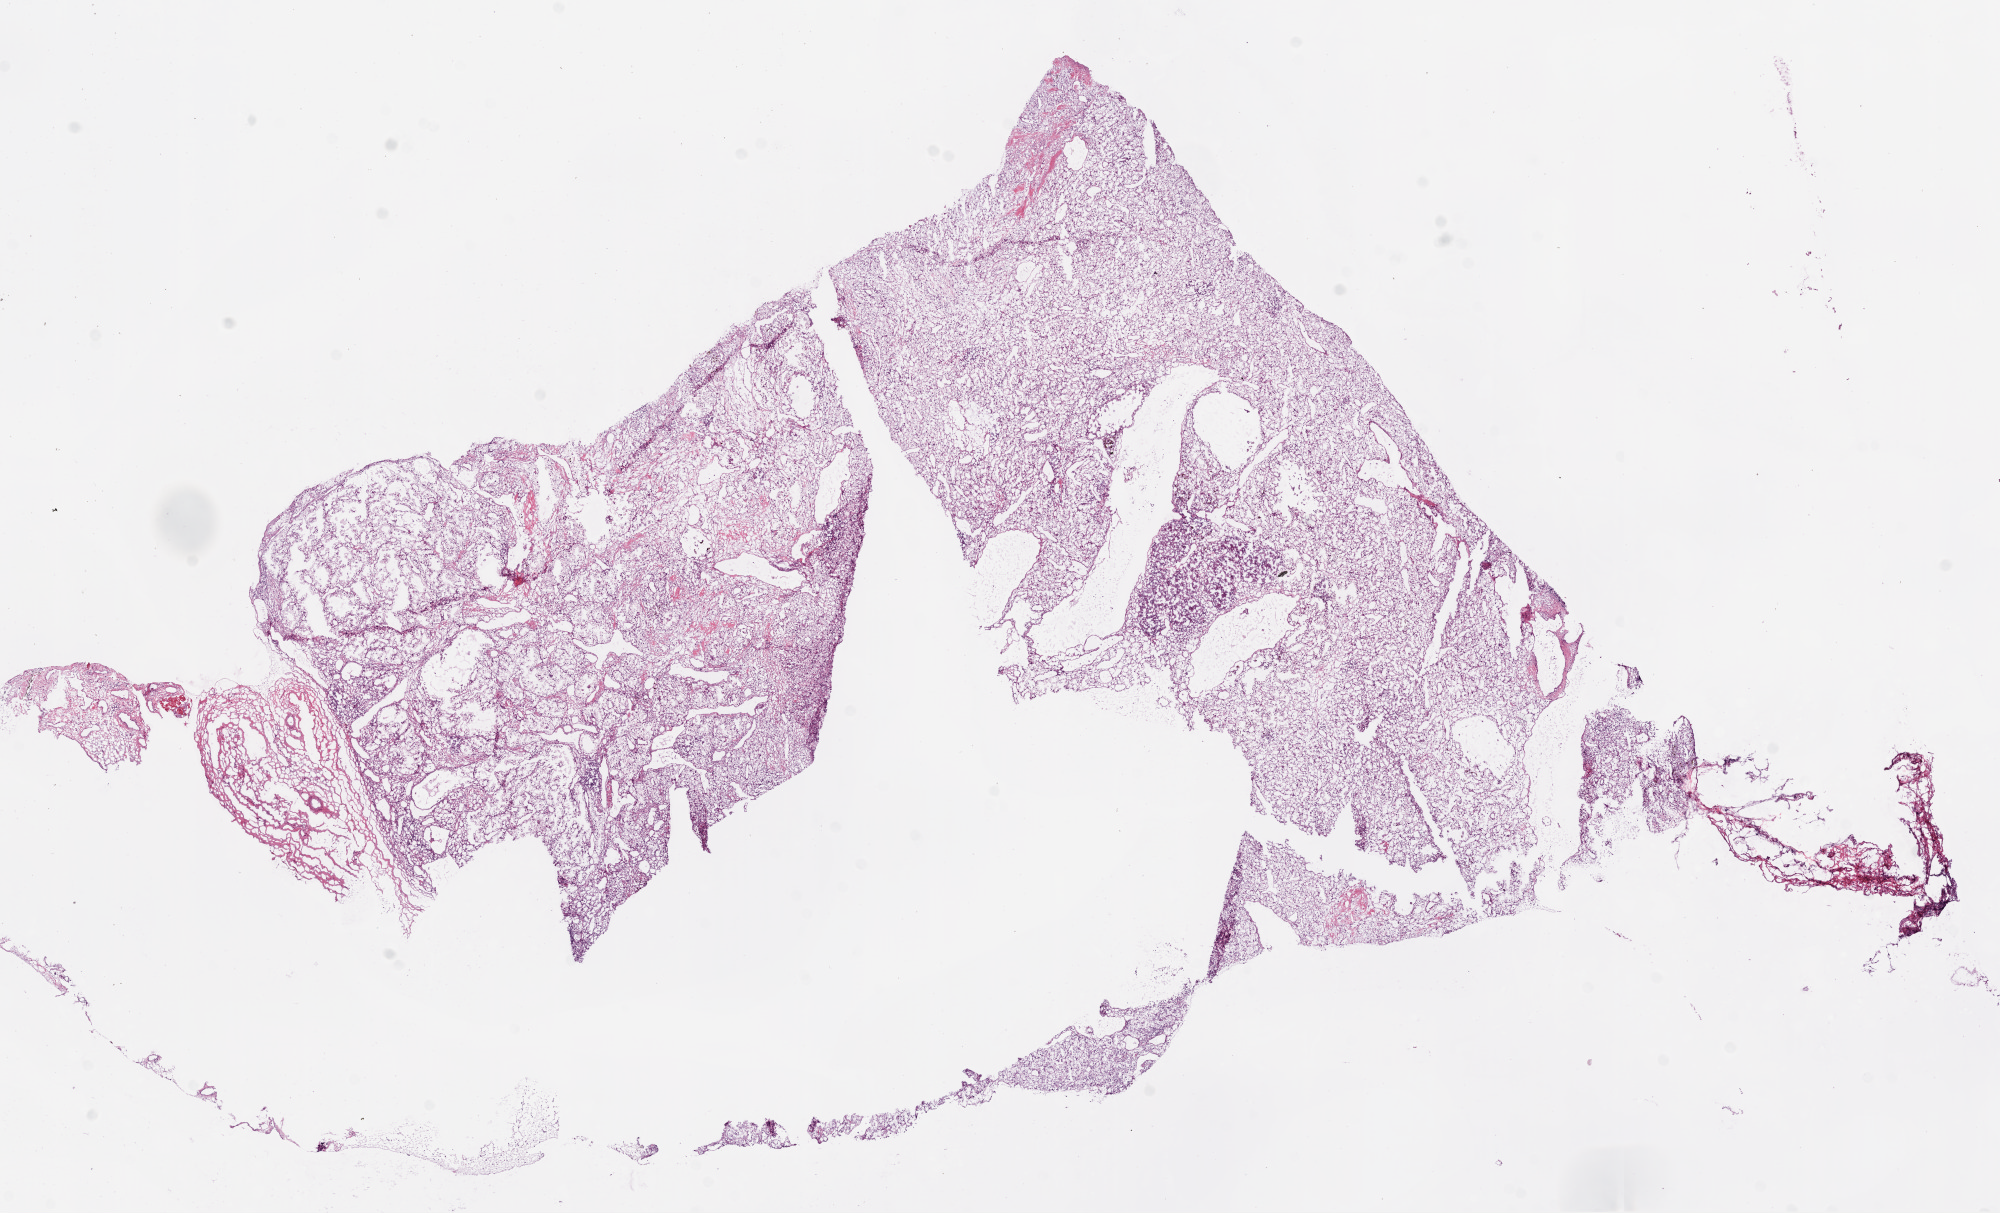
Hematoxylin and eosin (H&E) stained whole-slide image — whole scanned area (about 16.0 x 9.7 mm, slide scanned at 20x) shown as a low-resolution overview, frozen section, sample: primary tumour, kidney. Patient: male, age at initial diagnosis 76 years. Histologic grade: G2 (moderately differentiated). Pathologist review of this section (percent, as recorded): tumour cells 95%, tumour nuclei 99%, normal cells 0%, stromal cells 5%, necrosis 0%.
Histologic diagnosis: Clear cell adenocarcinoma, NOS. AJCC pathologic stage: I.